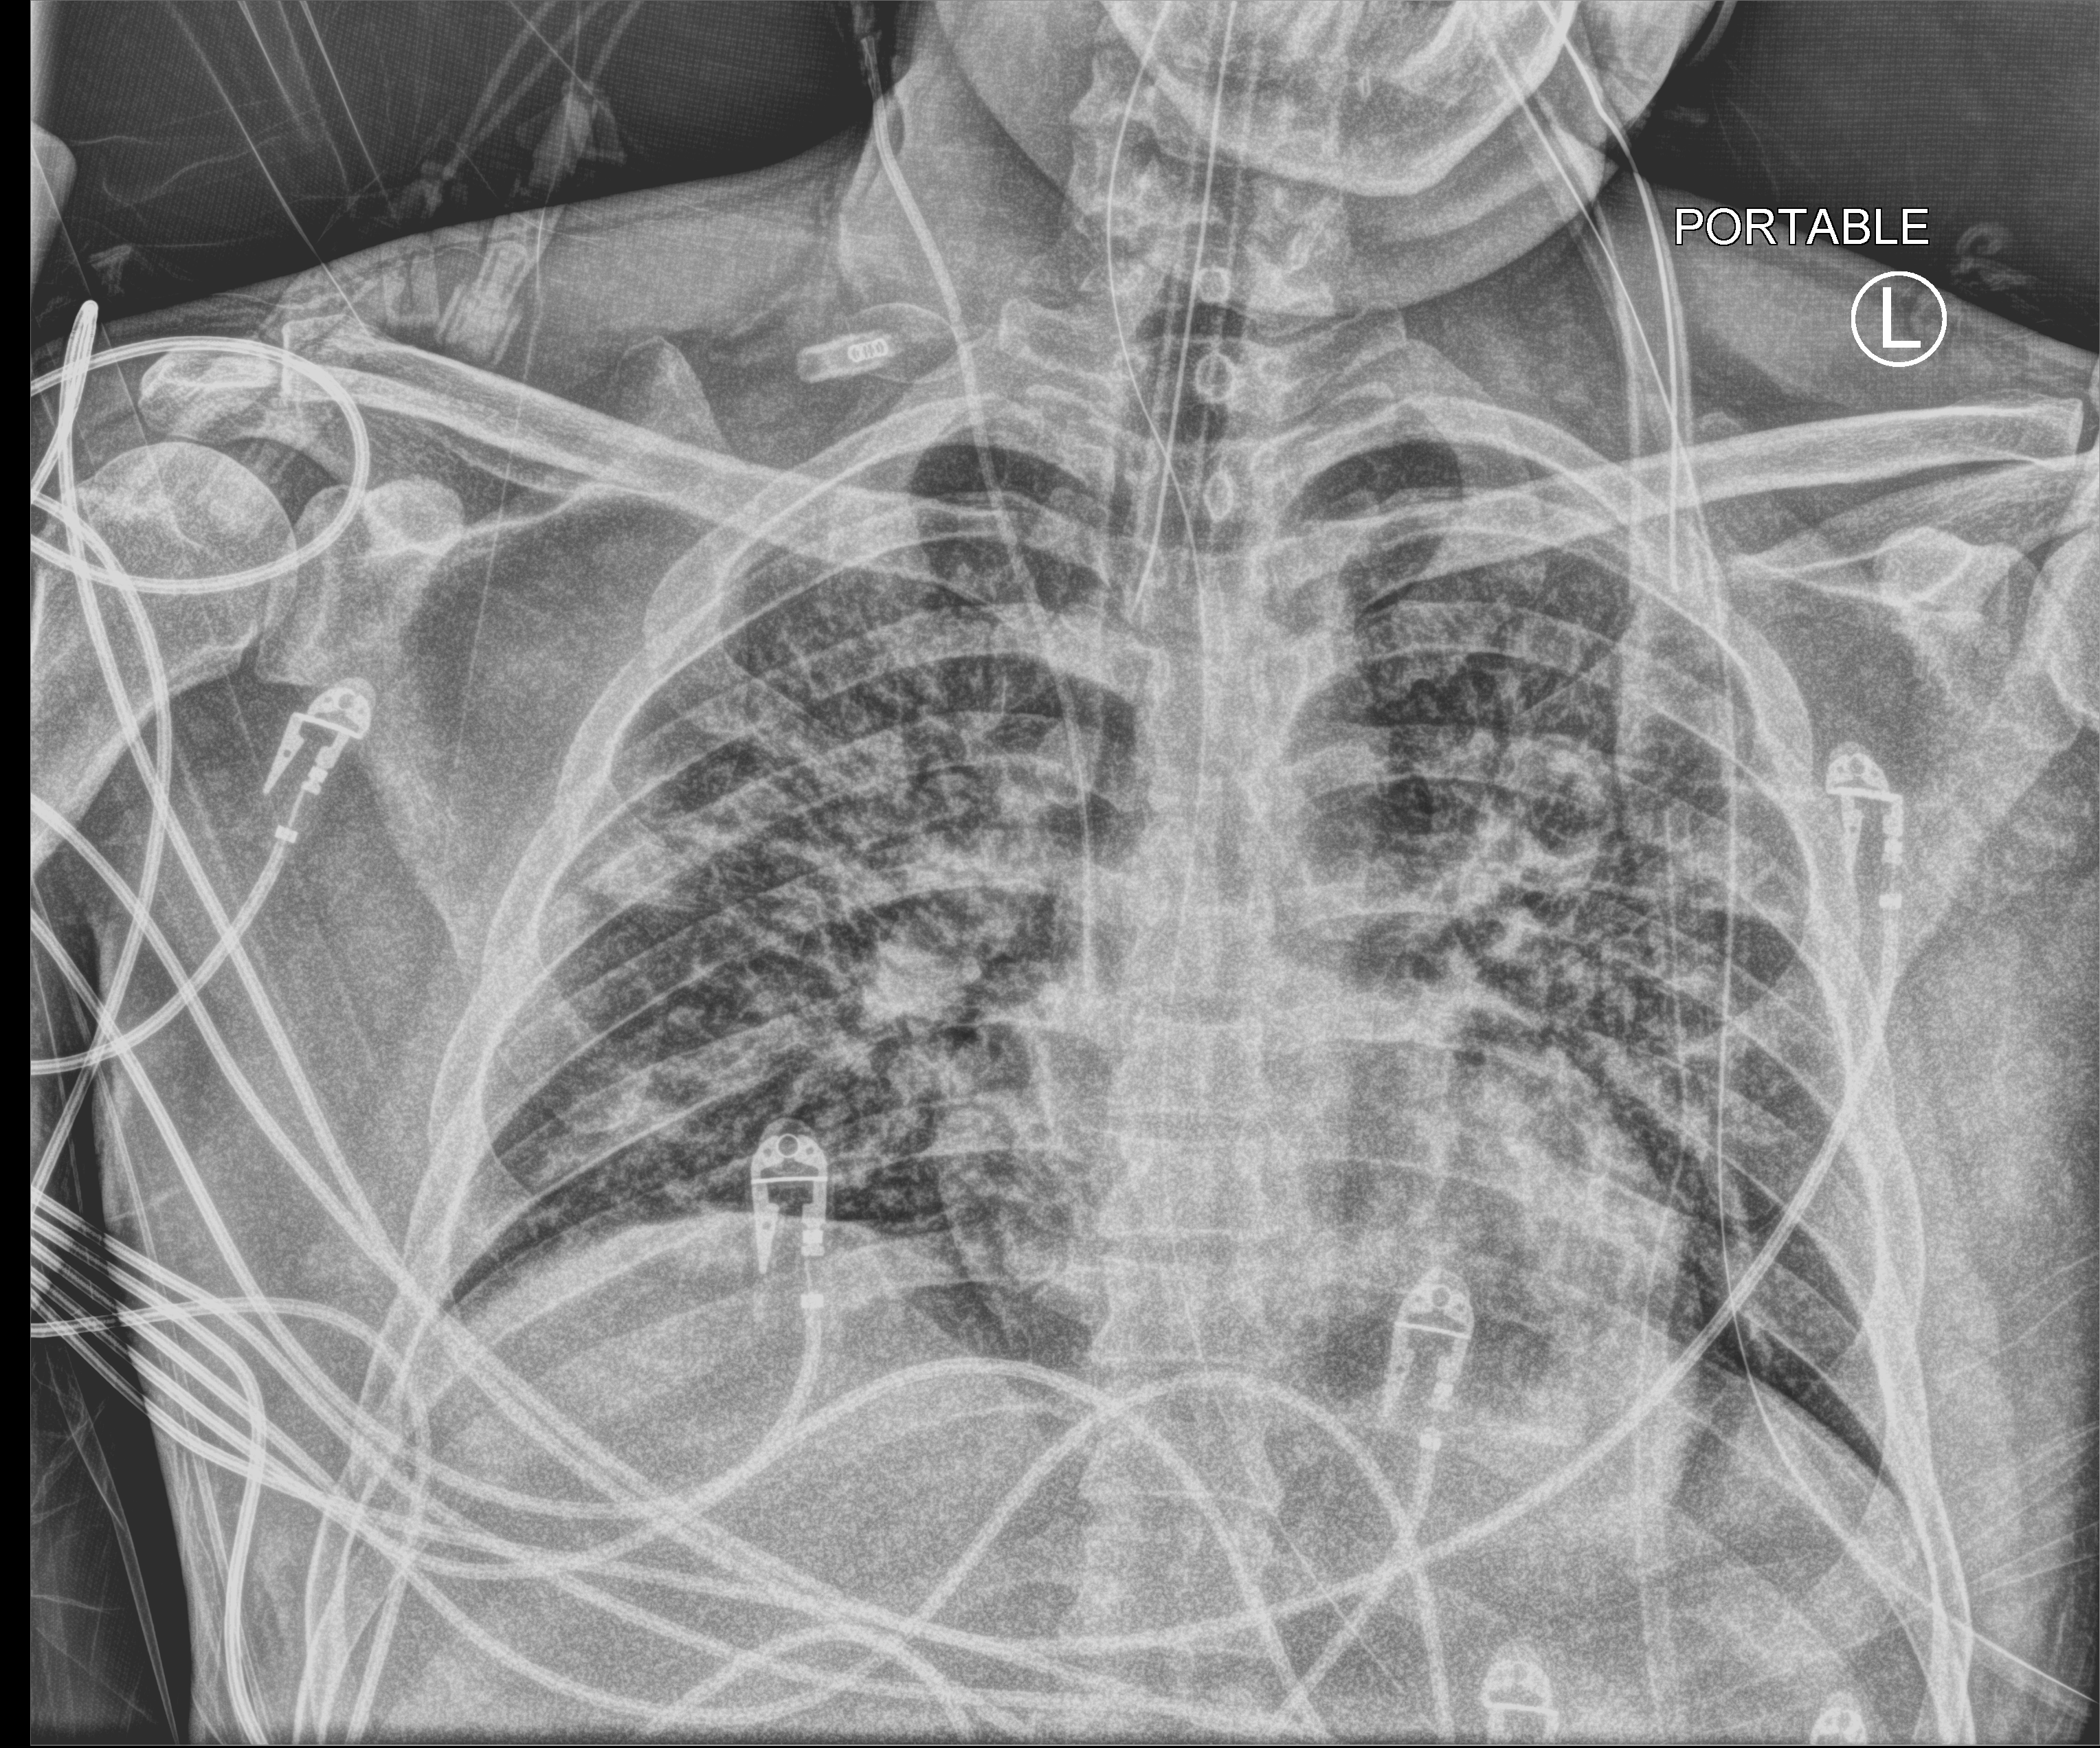
Portable chest radiograph, anteroposterior (AP) projection. Patient hospitalised with COVID-19; male, aged 18–59 years.
From the hospital-stay record, not from the radiograph (when in the stay this image was taken is not recorded):
- admitted to intensive care during this hospital stay: yes